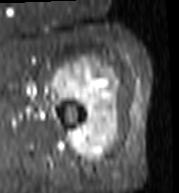
MRI of an extremity soft-tissue mass, one axial slice. Position 84 of 103 along the scan axis. STIR. MR volume resampled by the dataset authors to the PET/CT grid (not the native acquisition matrix). 3.27 mm slice thickness. 179 × 193 image matrix. Female patient. Case-level facts recorded for this patient, not image findings: histological type: undifferentiated – high grade; grade: high; site of the primary tumour: left thigh.
Annotated regions visible in this slice (expert contour drawn on MRI and transferred to this co-registered scan by the dataset authors):
- gross tumour volume including surrounding oedema: bounding box [x1, y1, x2, y2] px = [50, 57, 121, 163]
- gross tumour volume (mass): [52, 62, 119, 163]